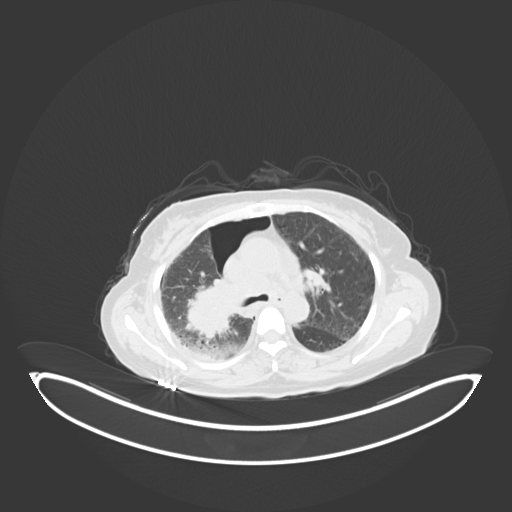
Chest CT, one axial slice; slice 38 of 69 in the series (ordered by position); 120 kVp; lung window (W 1500 / L -600 HU); 512 × 512 image matrix, field of view 500 × 500 mm. Female patient, age 64 years. From the clinical record (not read from this slice): clinical TNM (as recorded): T3 N3 M0.
Structures marked on this image (rectangle marked by the reading radiologist):
- lung tumour (recorded histology: squamous cell carcinoma): box from (x=179, y=275) to (x=243, y=346) px